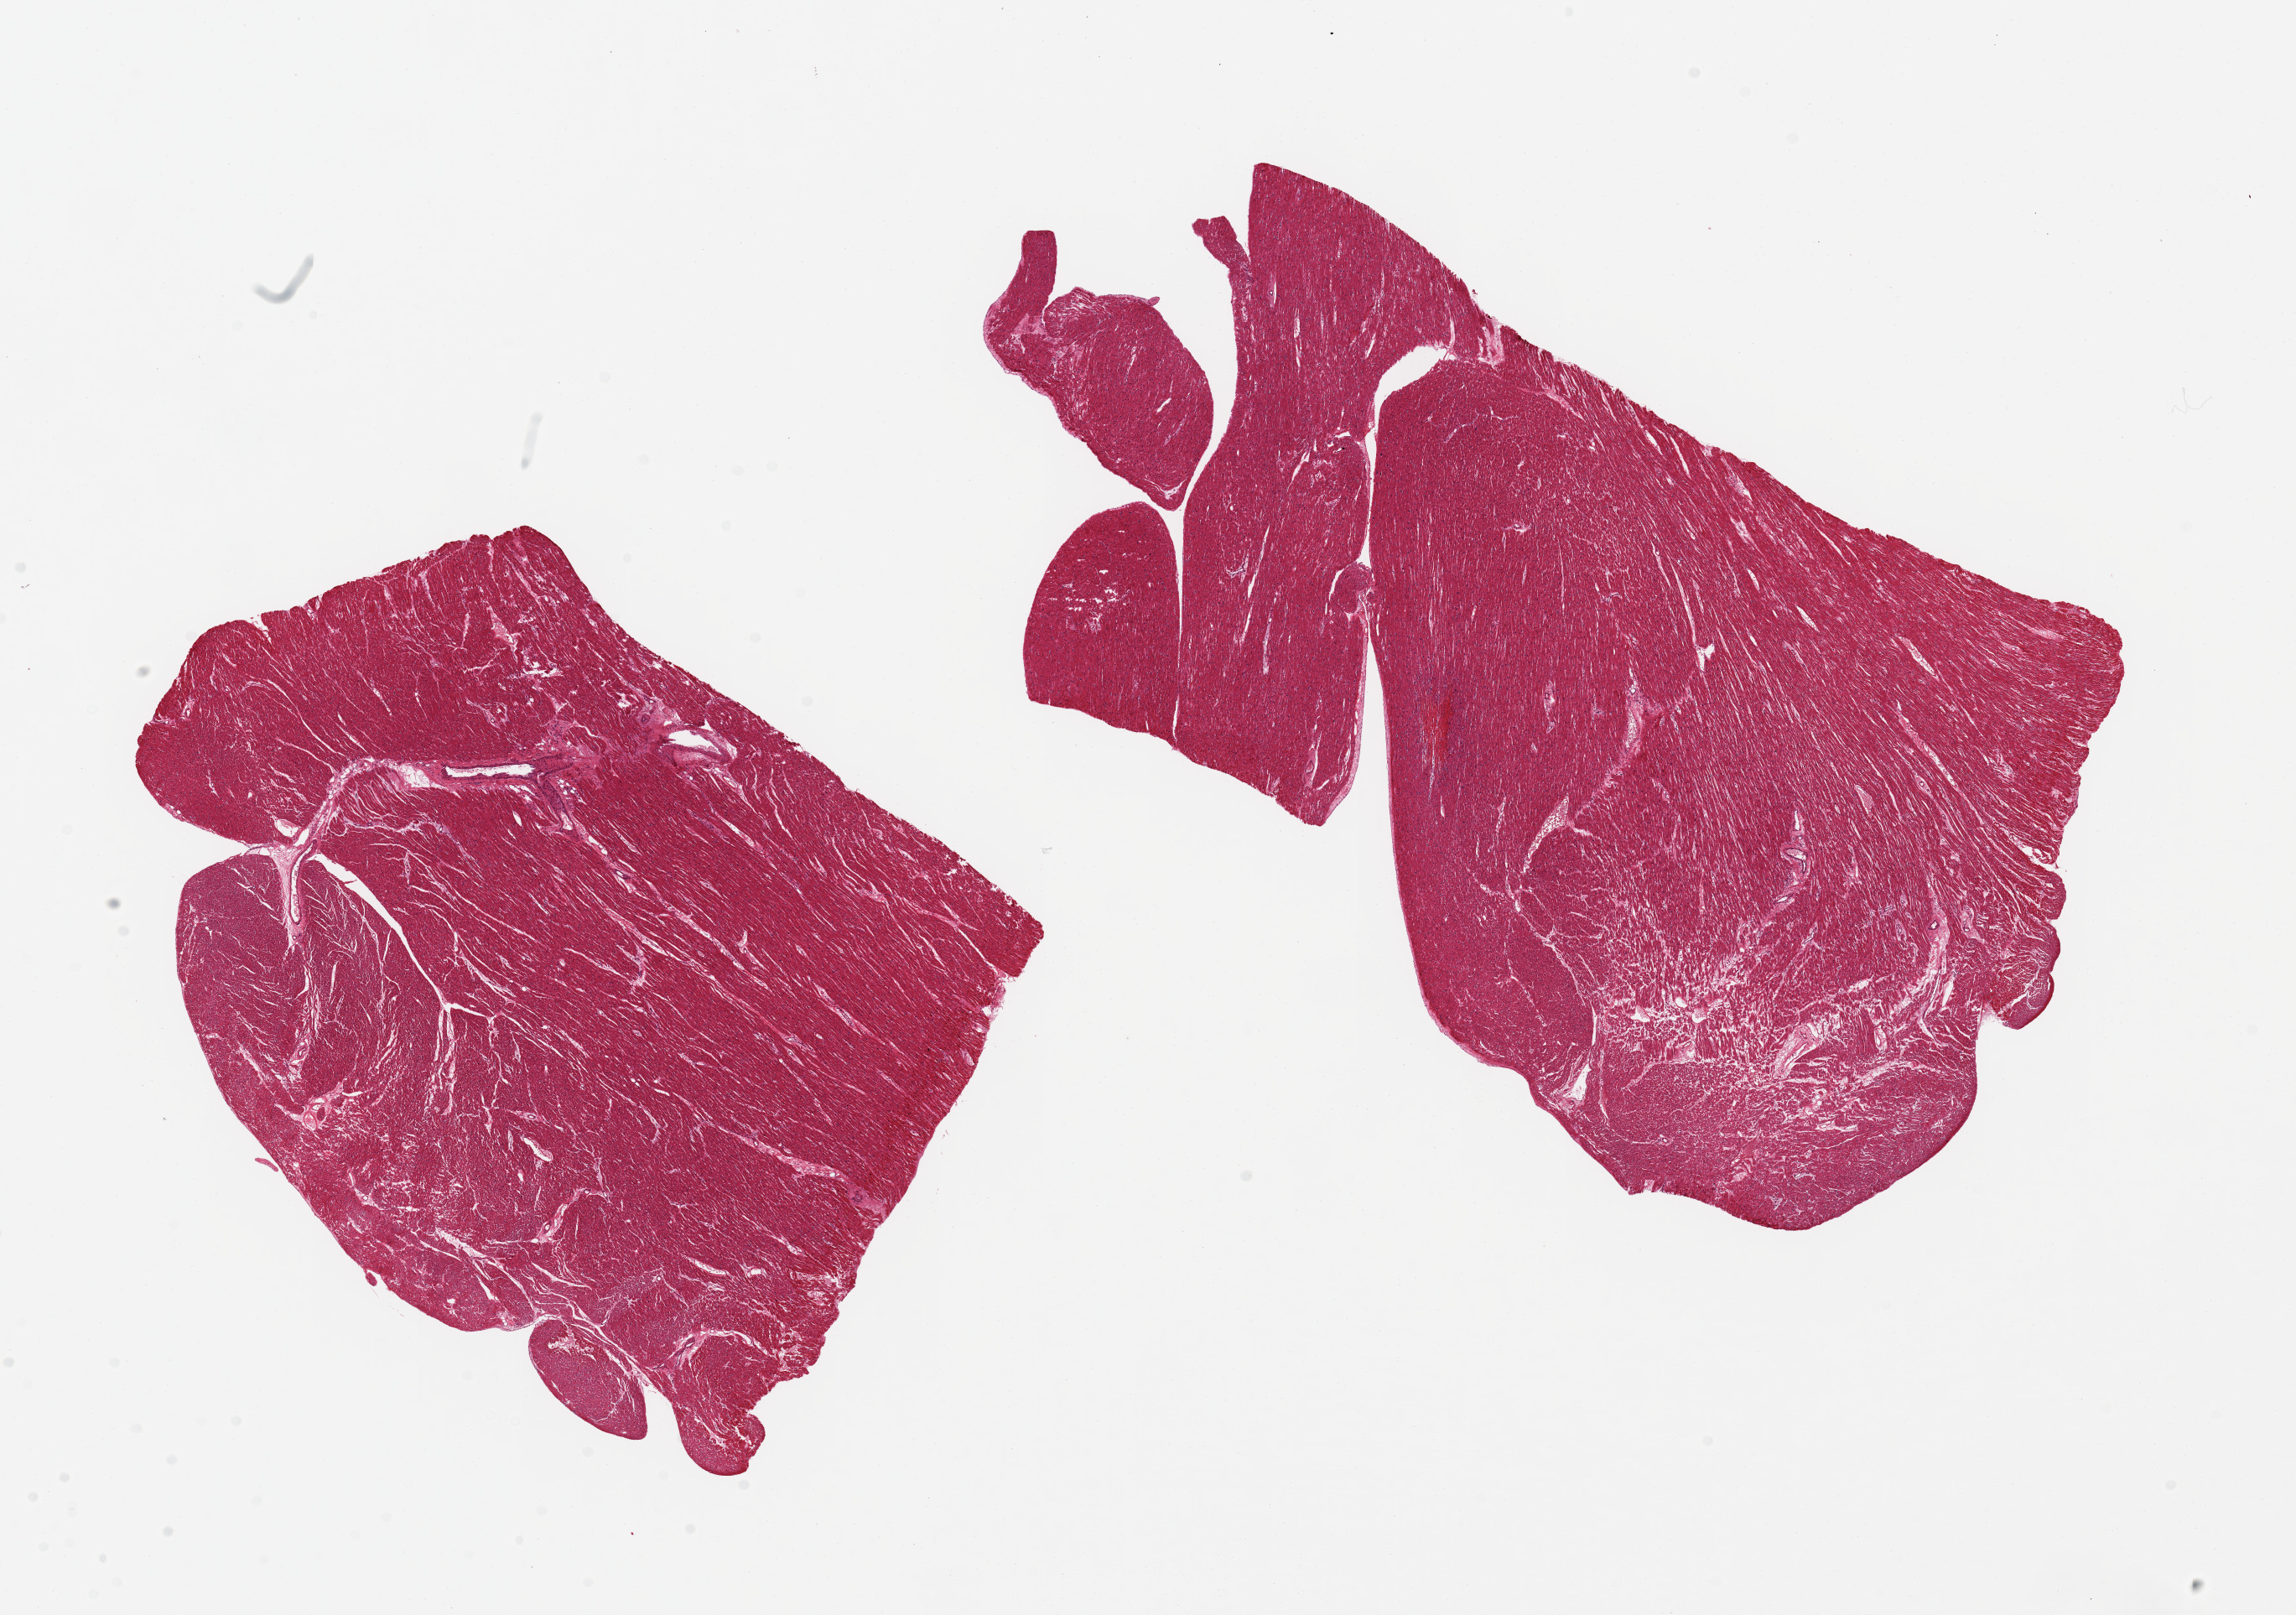
Hematoxylin and eosin (H&E) whole-slide image, shown as a low-resolution overview of the whole scanned area (about 21.7 x 15.2 mm). PAXgene-fixed, paraffin-embedded tissue. Sampled site (target tissue): heart. Tissue donor sample.
Reviewer comment on this tissue sample: 2 pieces 9x7 & 7x6 mm; good clean specimen; papillary muscles with endothelium.